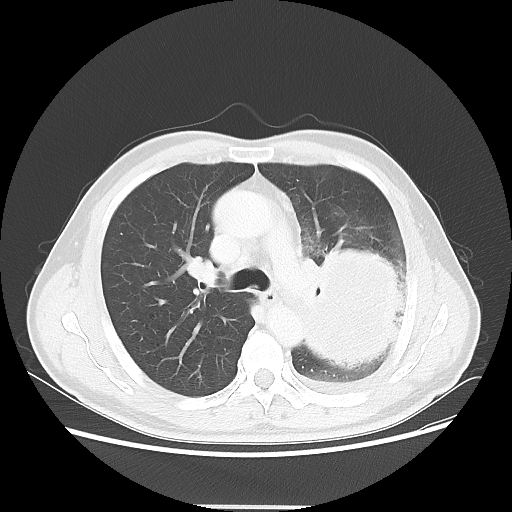
Chest CT, one axial slice; slice 35 of 53 in the series (ordered by position); 100 kVp; lung window (W 1500 / L -600 HU); 5 mm slice thickness; 512 × 512 image matrix. Patient: male, 60 years. From the clinical record (not read from this slice): clinical TNM (as recorded): T4 N1 M1a.
Outlined on this slice (bounding box drawn by a radiologist):
- lung tumour (recorded histology: large cell carcinoma): box from (x=302, y=247) to (x=405, y=371) px